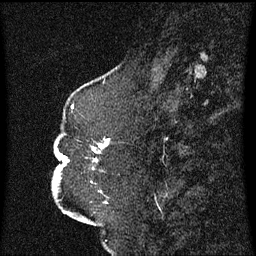
Breast MRI (dynamic contrast-enhanced), one sagittal slice. Slice 24 of 60 in the series (ordered by position). Dynamic contrast-enhanced series, image 2 of 3 at this slice position (ordered by acquisition). 1.5 T. TE 4.2 ms, TR 8.4 ms. 2.3 mm slice thickness. 256 × 256 image matrix, field of view 200 × 200 mm. Patient: female, 52 years. Case-level facts recorded for this patient, not image findings: setting: breast cancer imaged before/during neoadjuvant chemotherapy; receptor status: HR-positive, HER2-negative.
Annotated regions visible in this slice (semi-automatic segmentation, software-assisted and operator-edited):
- analysis volume of interest (the breast-tissue region the enhancement analysis was run in; not a lesion): bounding box (x1, y1, x2, y2) in pixels: (52, 128, 108, 197)
- tumour enhancement mask (voxels above the 70 % enhancement threshold inside the analysis volume of interest): (68, 142, 108, 163)